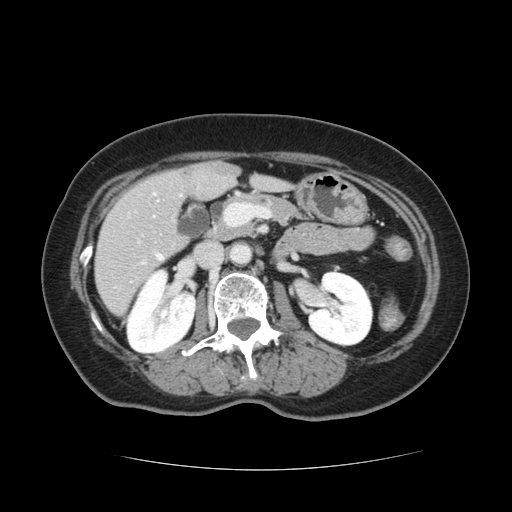
Contrast-enhanced abdominal CT, one axial slice. Position 50 of 128 along the scan axis. 120 kVp. Intravenous contrast given. Soft-tissue window (W 400 / L 40 HU). 512 × 512 image matrix, field of view 366 × 366 mm. Female patient, age 67 years. Case-level facts recorded for this patient, not image findings: diagnosis: colorectal cancer liver metastases, imaged before liver resection; multiple liver metastases: yes; largest metastasis: 3 cm; disease in both lobes: yes.
Structures marked on this image (outlined manually by an expert reader):
- hepatic veins: bounding box (x1, y1, x2, y2) in pixels: (116, 254, 164, 288)
- liver: (96, 163, 284, 315)
- planned liver remnant (the part of the liver to remain after resection): (96, 175, 285, 314)
- portal vein (with intrahepatic branches): (136, 205, 242, 264)